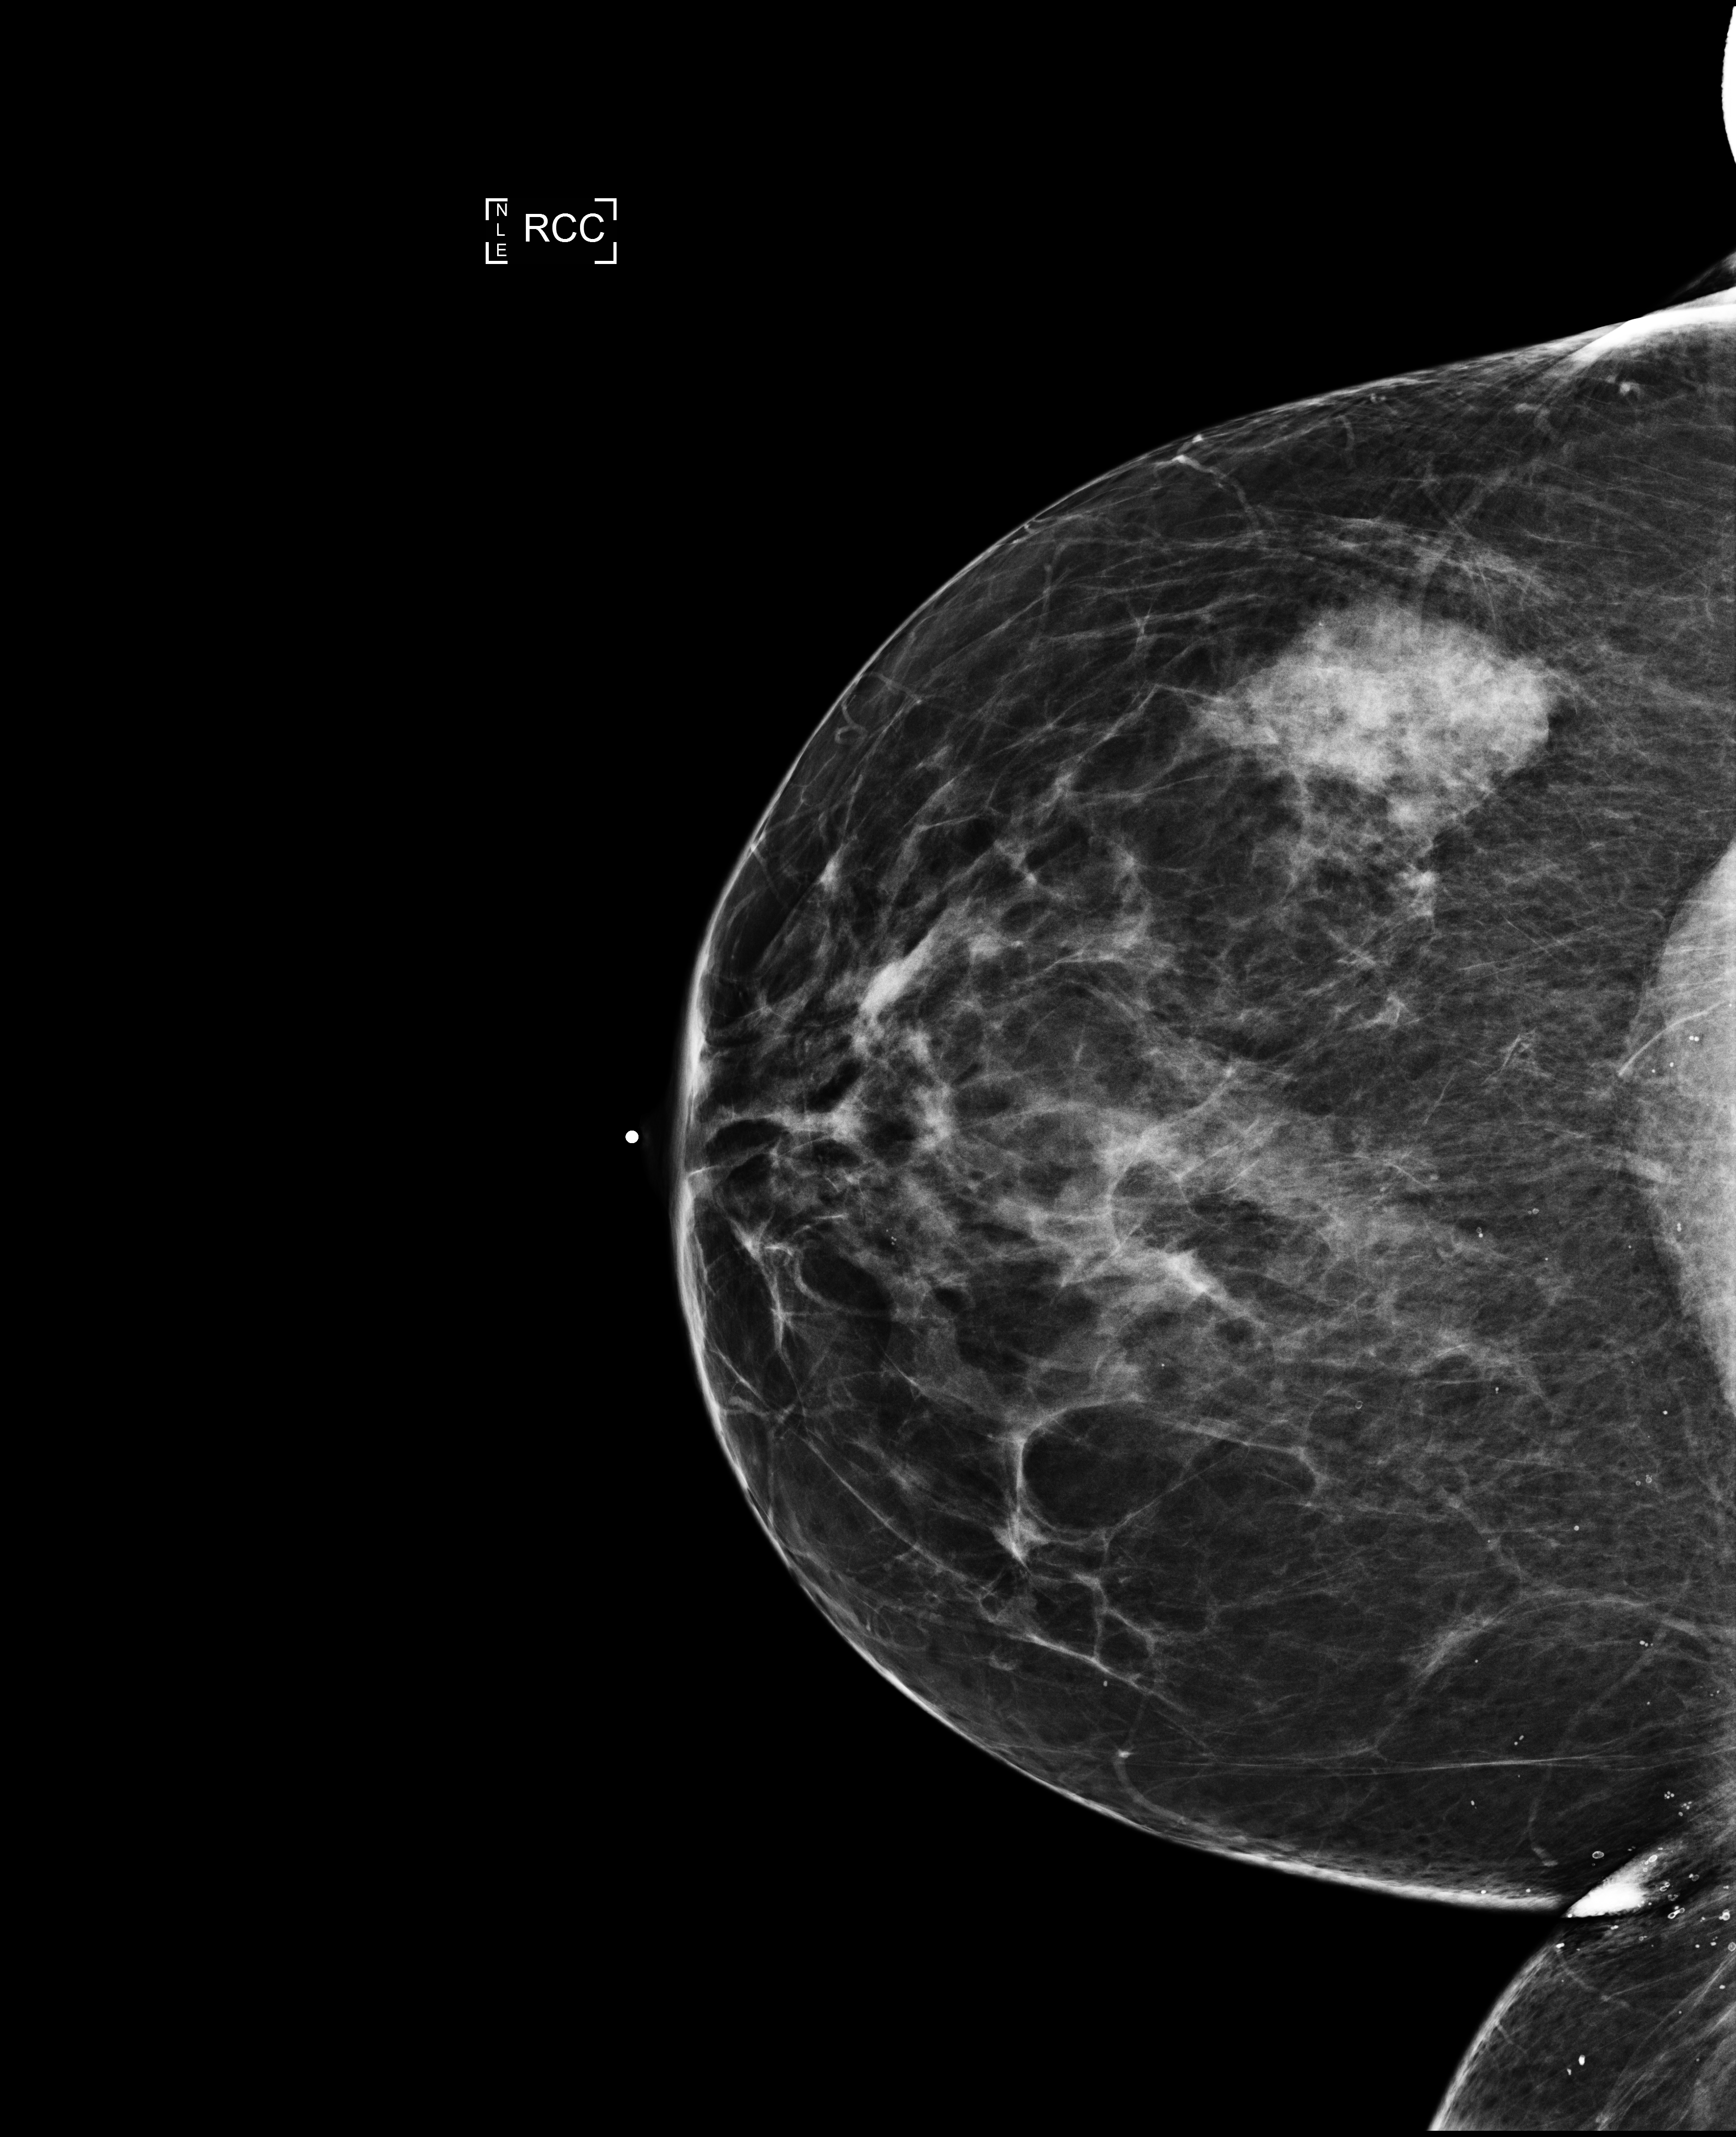
Annual screening mammography examination, compressed breast thickness 62 mm. Patient: female, 61 years.
Image type: full-field digital mammogram. Breast: right. Projection: cranio-caudal projection.